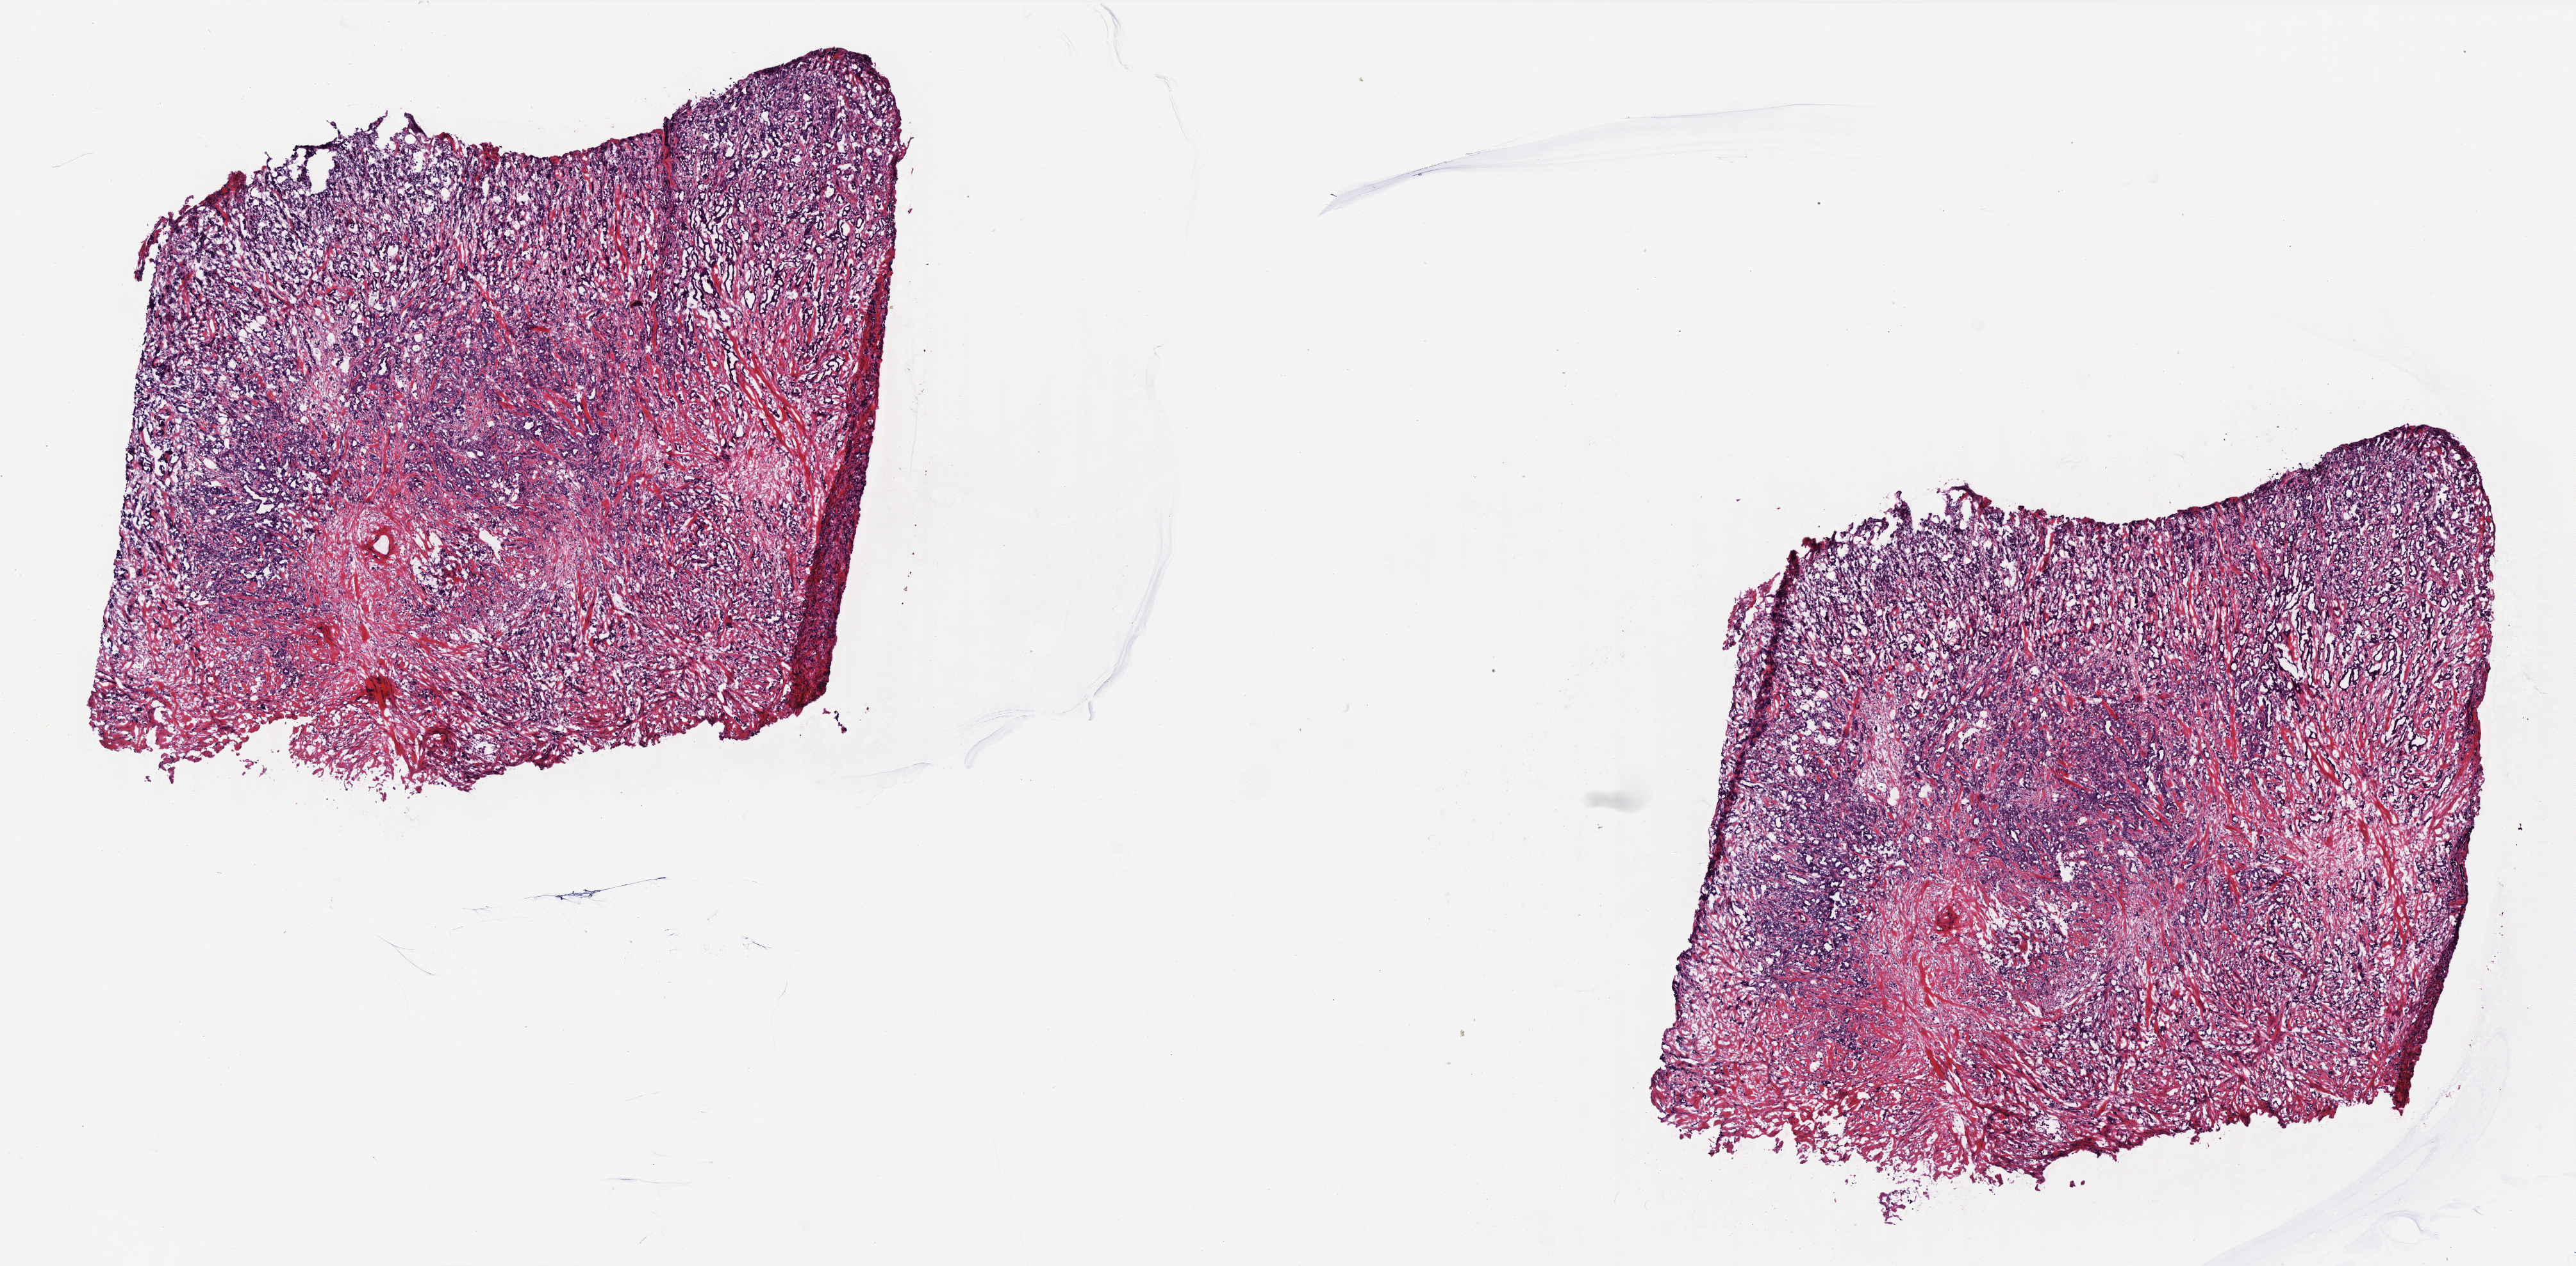
H&E whole-slide image, shown as a low-resolution overview of the whole scanned area (about 16.1 x 7.9 mm); frozen section from the top of the tissue portion; breast, primary tumour sample. Female patient; age at initial diagnosis 70 years. Pathologist review of this section (percent, as recorded): tumour cells 70%, tumour nuclei 88%, normal cells 0%, stromal cells 28%, necrosis 2%. Infiltration values recorded for this section: lymphocyte infiltration 5%, monocyte infiltration 1%, neutrophil infiltration 0%.
Lymph nodes positive (case pathology): 4 of 9 examined. AJCC pathologic stage: IIIA. Histologic diagnosis: Infiltrating duct carcinoma, NOS. TNM: T2 N2 M0.